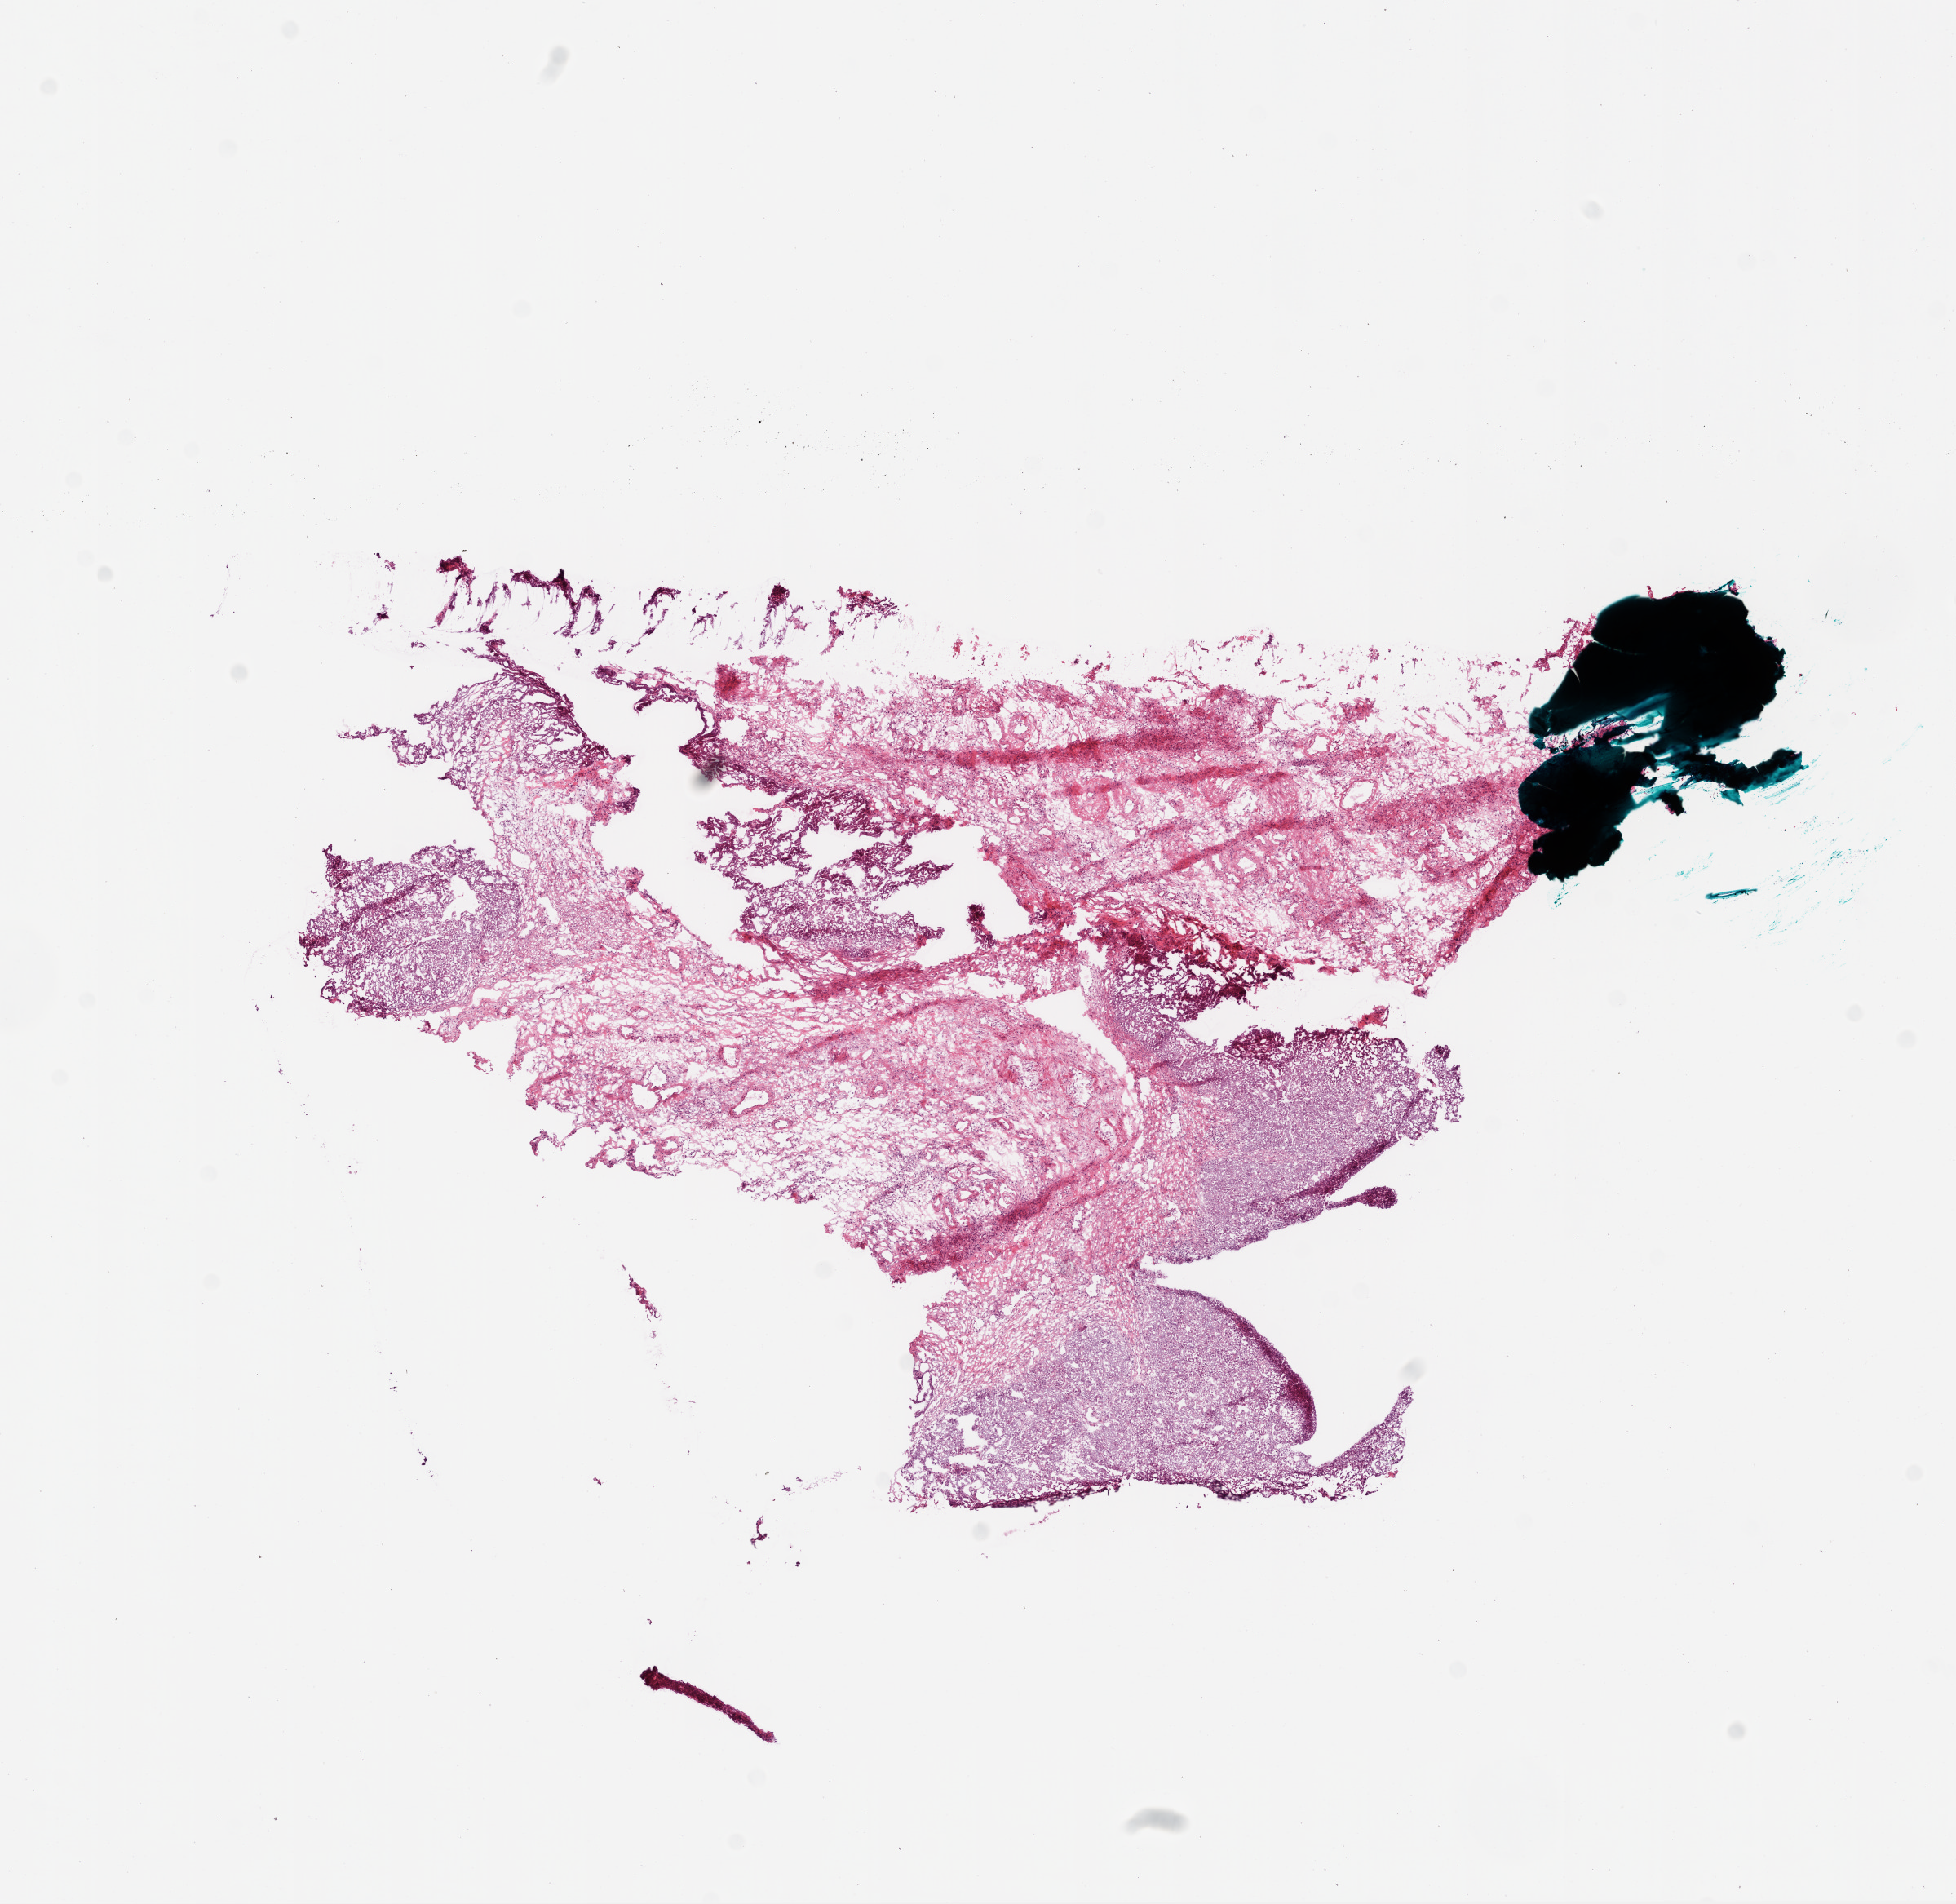
Whole-slide histology image, Hematoxylin and eosin (H&E) stained, low-resolution overview of the scanned area, about 9.7 x 9.4 mm; frozen section; ovary, primary tumour sample. Female, age 65 years at initial diagnosis. Histologic grade: G3 (poorly differentiated). Pathologist review of this section (percent, as recorded): tumour cells 70%, tumour nuclei 80%, normal cells 5%, stromal cells 5%, necrosis 20%.
FIGO stage: IIIC. Laterality: right. Histologic diagnosis: Serous cystadenocarcinoma, NOS.